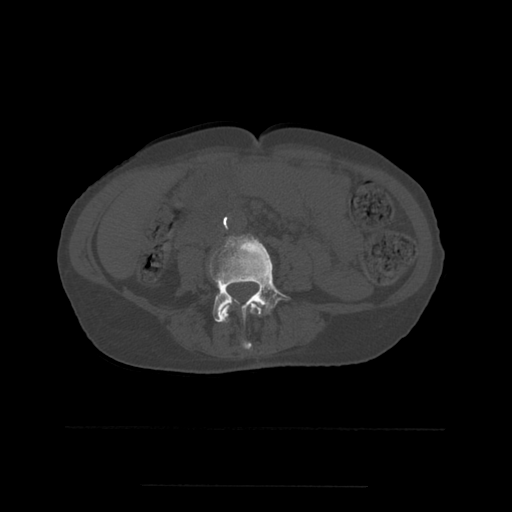
CT including the spine, one axial slice; slice 173 of 544 in the series (ordered by position); bone window (W 1800 / L 400 HU); 512 × 512 image matrix, field of view 350 × 350 mm. Patient age 58 years. From the clinical record (not read from this slice): primary cancer: lung.
Annotated regions visible in this slice (semi-automatic segmentation, software-assisted and operator-edited):
- L3 vertebra: bounding box [x1, y1, x2, y2] px = [218, 301, 263, 350]
- L4 vertebra: [210, 234, 291, 322]